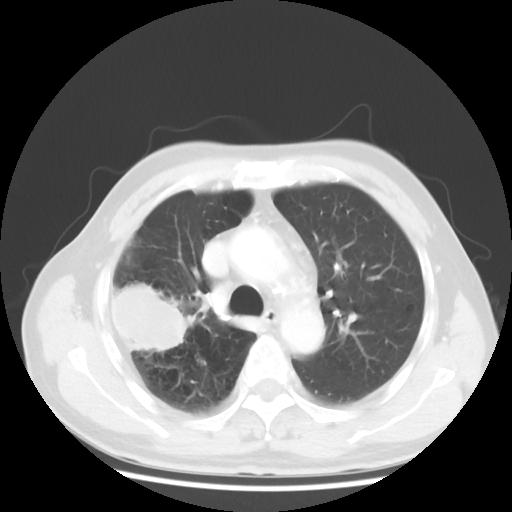
Chest CT, one axial slice. Position 35 of 50 along the scan axis. Lung window (W 1500 / L -600 HU). 5 mm slice thickness. 512 × 512 image matrix. Patient: male, 69 years. Case-level facts recorded for this patient, not image findings: clinical TNM (as recorded): T3 N0 M0; histopathological grade: G3.
Annotated regions visible in this slice (bounding box drawn by a radiologist):
- lung tumour (recorded histology: adenocarcinoma): bounding box (x1, y1, x2, y2) in pixels: (107, 275, 191, 354)